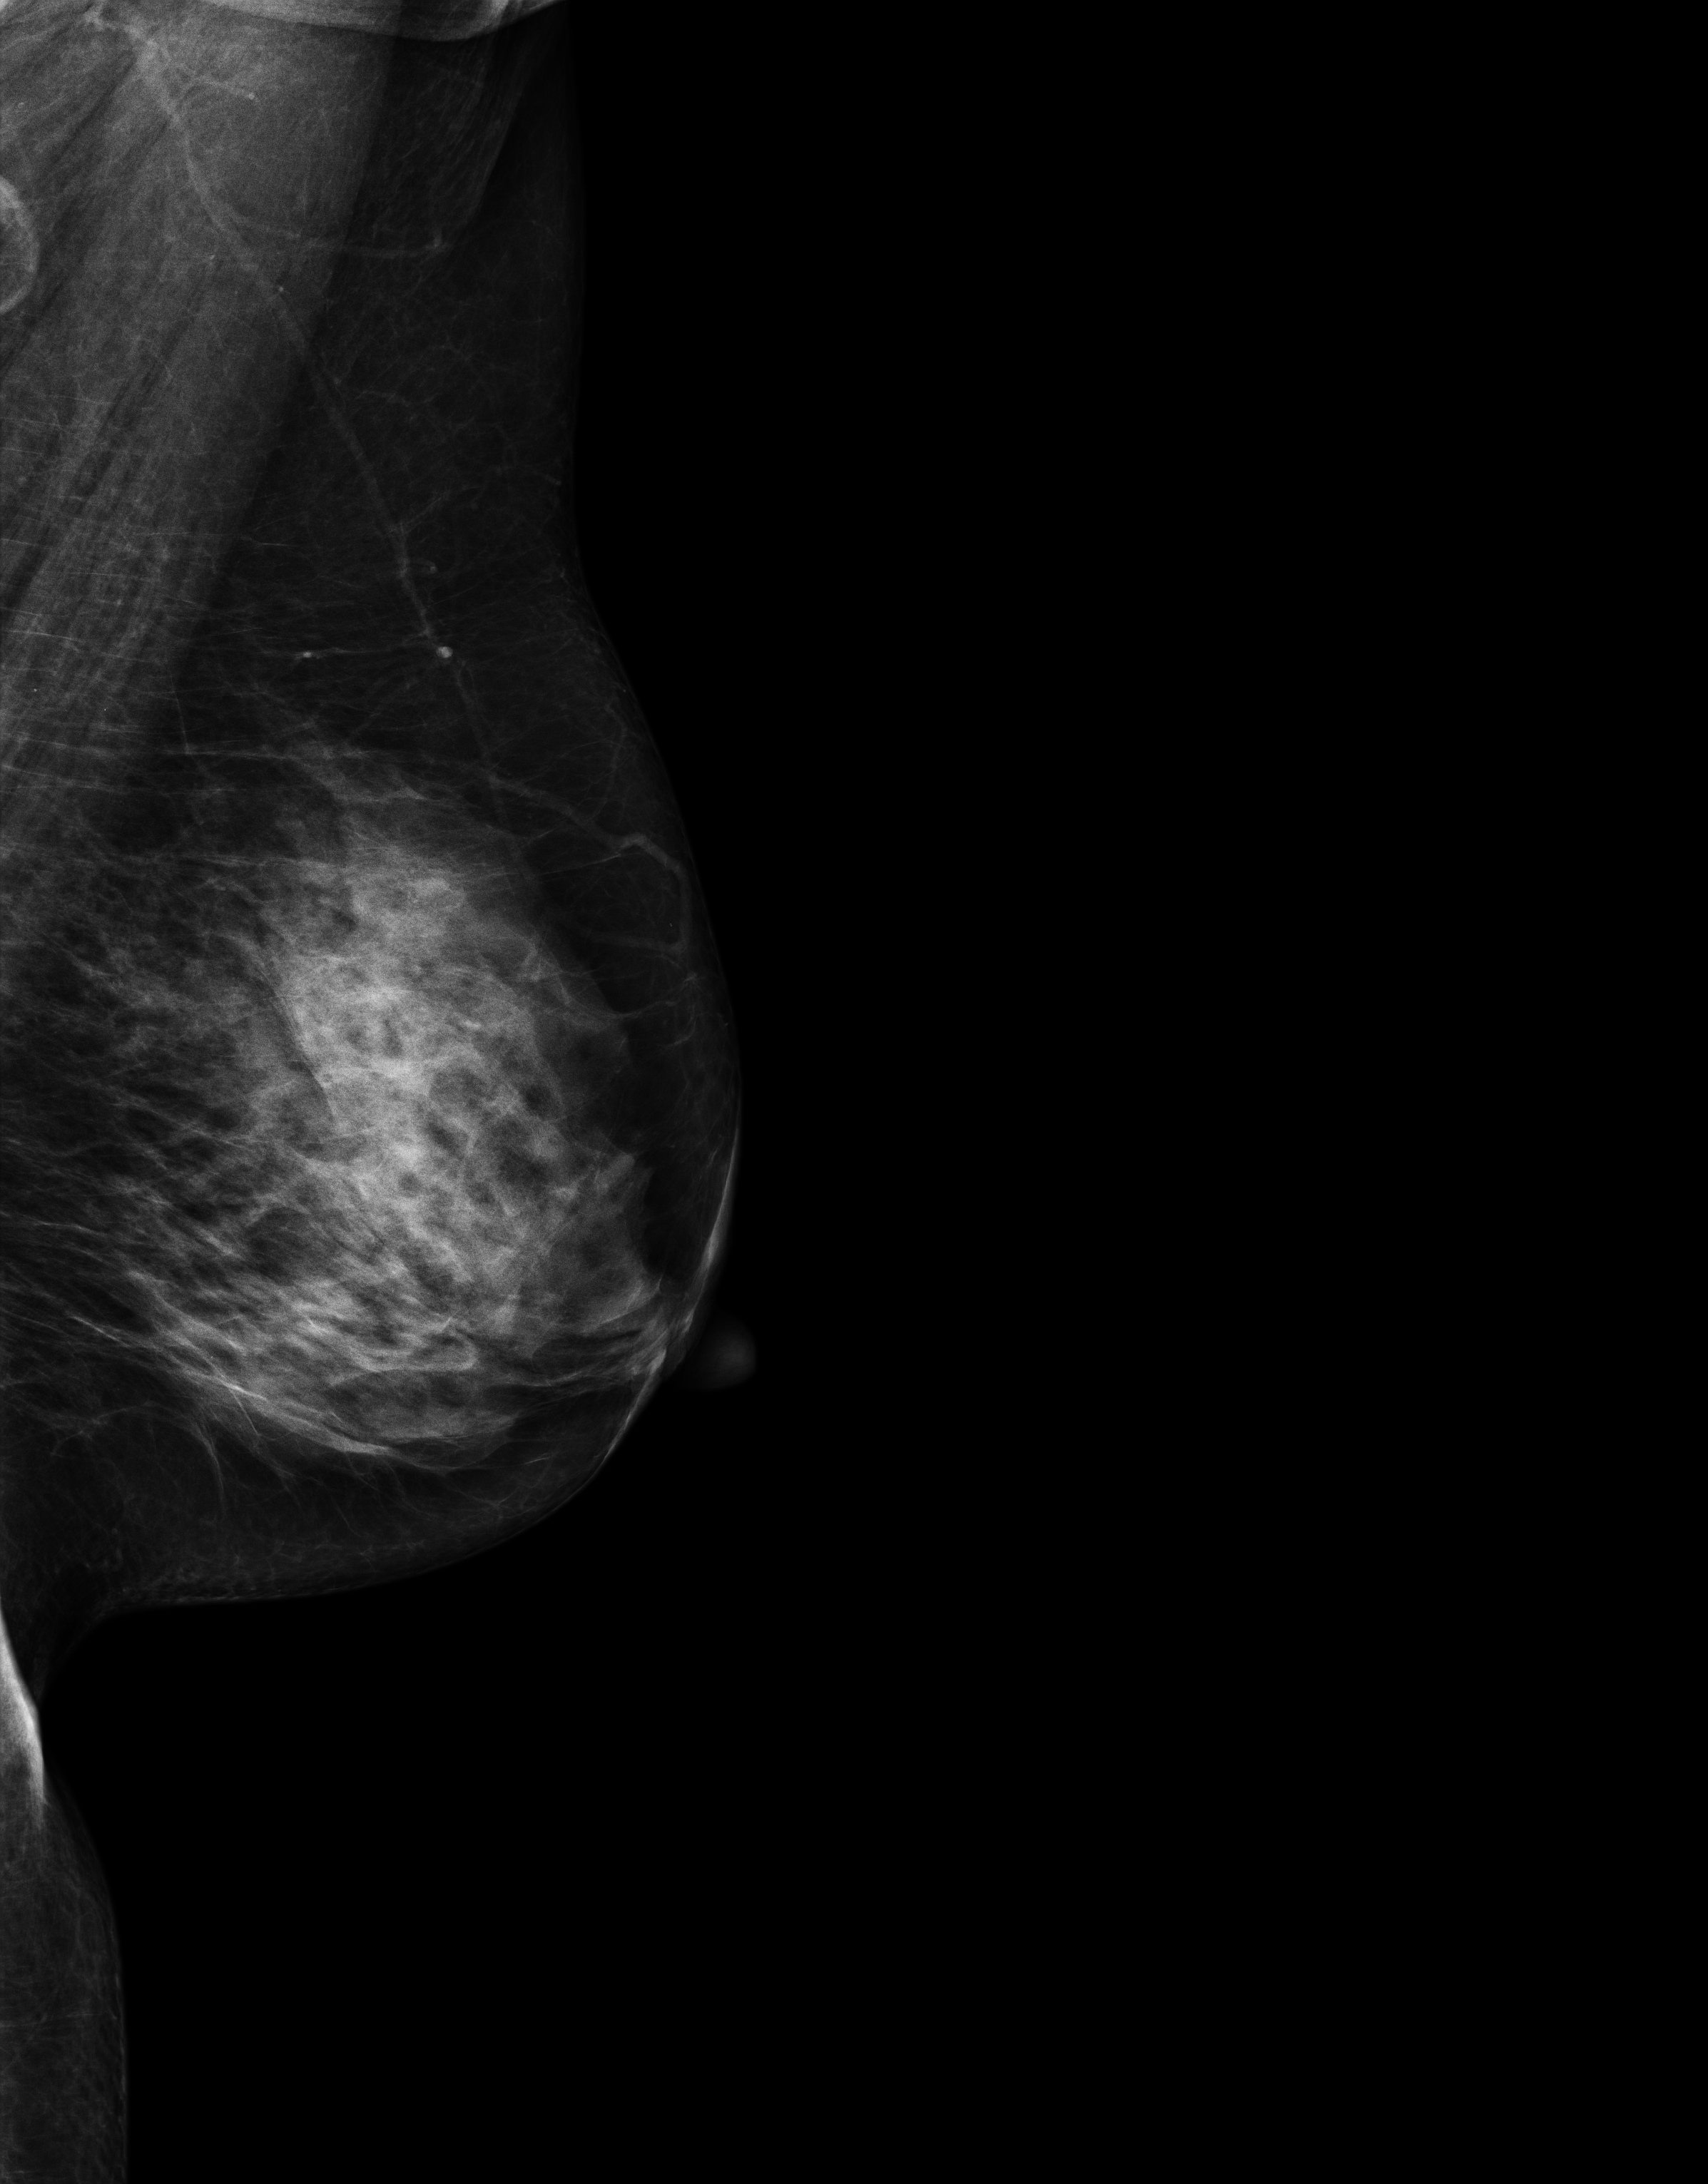
Screening examination; compressed breast thickness 64 mm. Female patient, age 67 years.
Image type: full-field digital mammogram. Breast: left. Projection: mediolateral oblique (MLO) view.